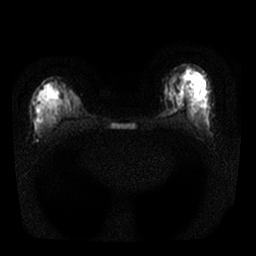
Breast MRI, one axial slice; slice 7 of 25 in the series (ordered by position); diffusion-weighted series; image 2 of 4 stored at this slice position (different b-values; order by instance number); 1.5 T; 4 mm slice thickness; 256 × 256 image matrix, field of view 320 × 320 mm. Female patient.
Outlined on this slice (expert manual segmentation):
- tumour on diffusion-weighted imaging: bounding box (x1, y1, x2, y2) in pixels: (201, 116, 203, 119)